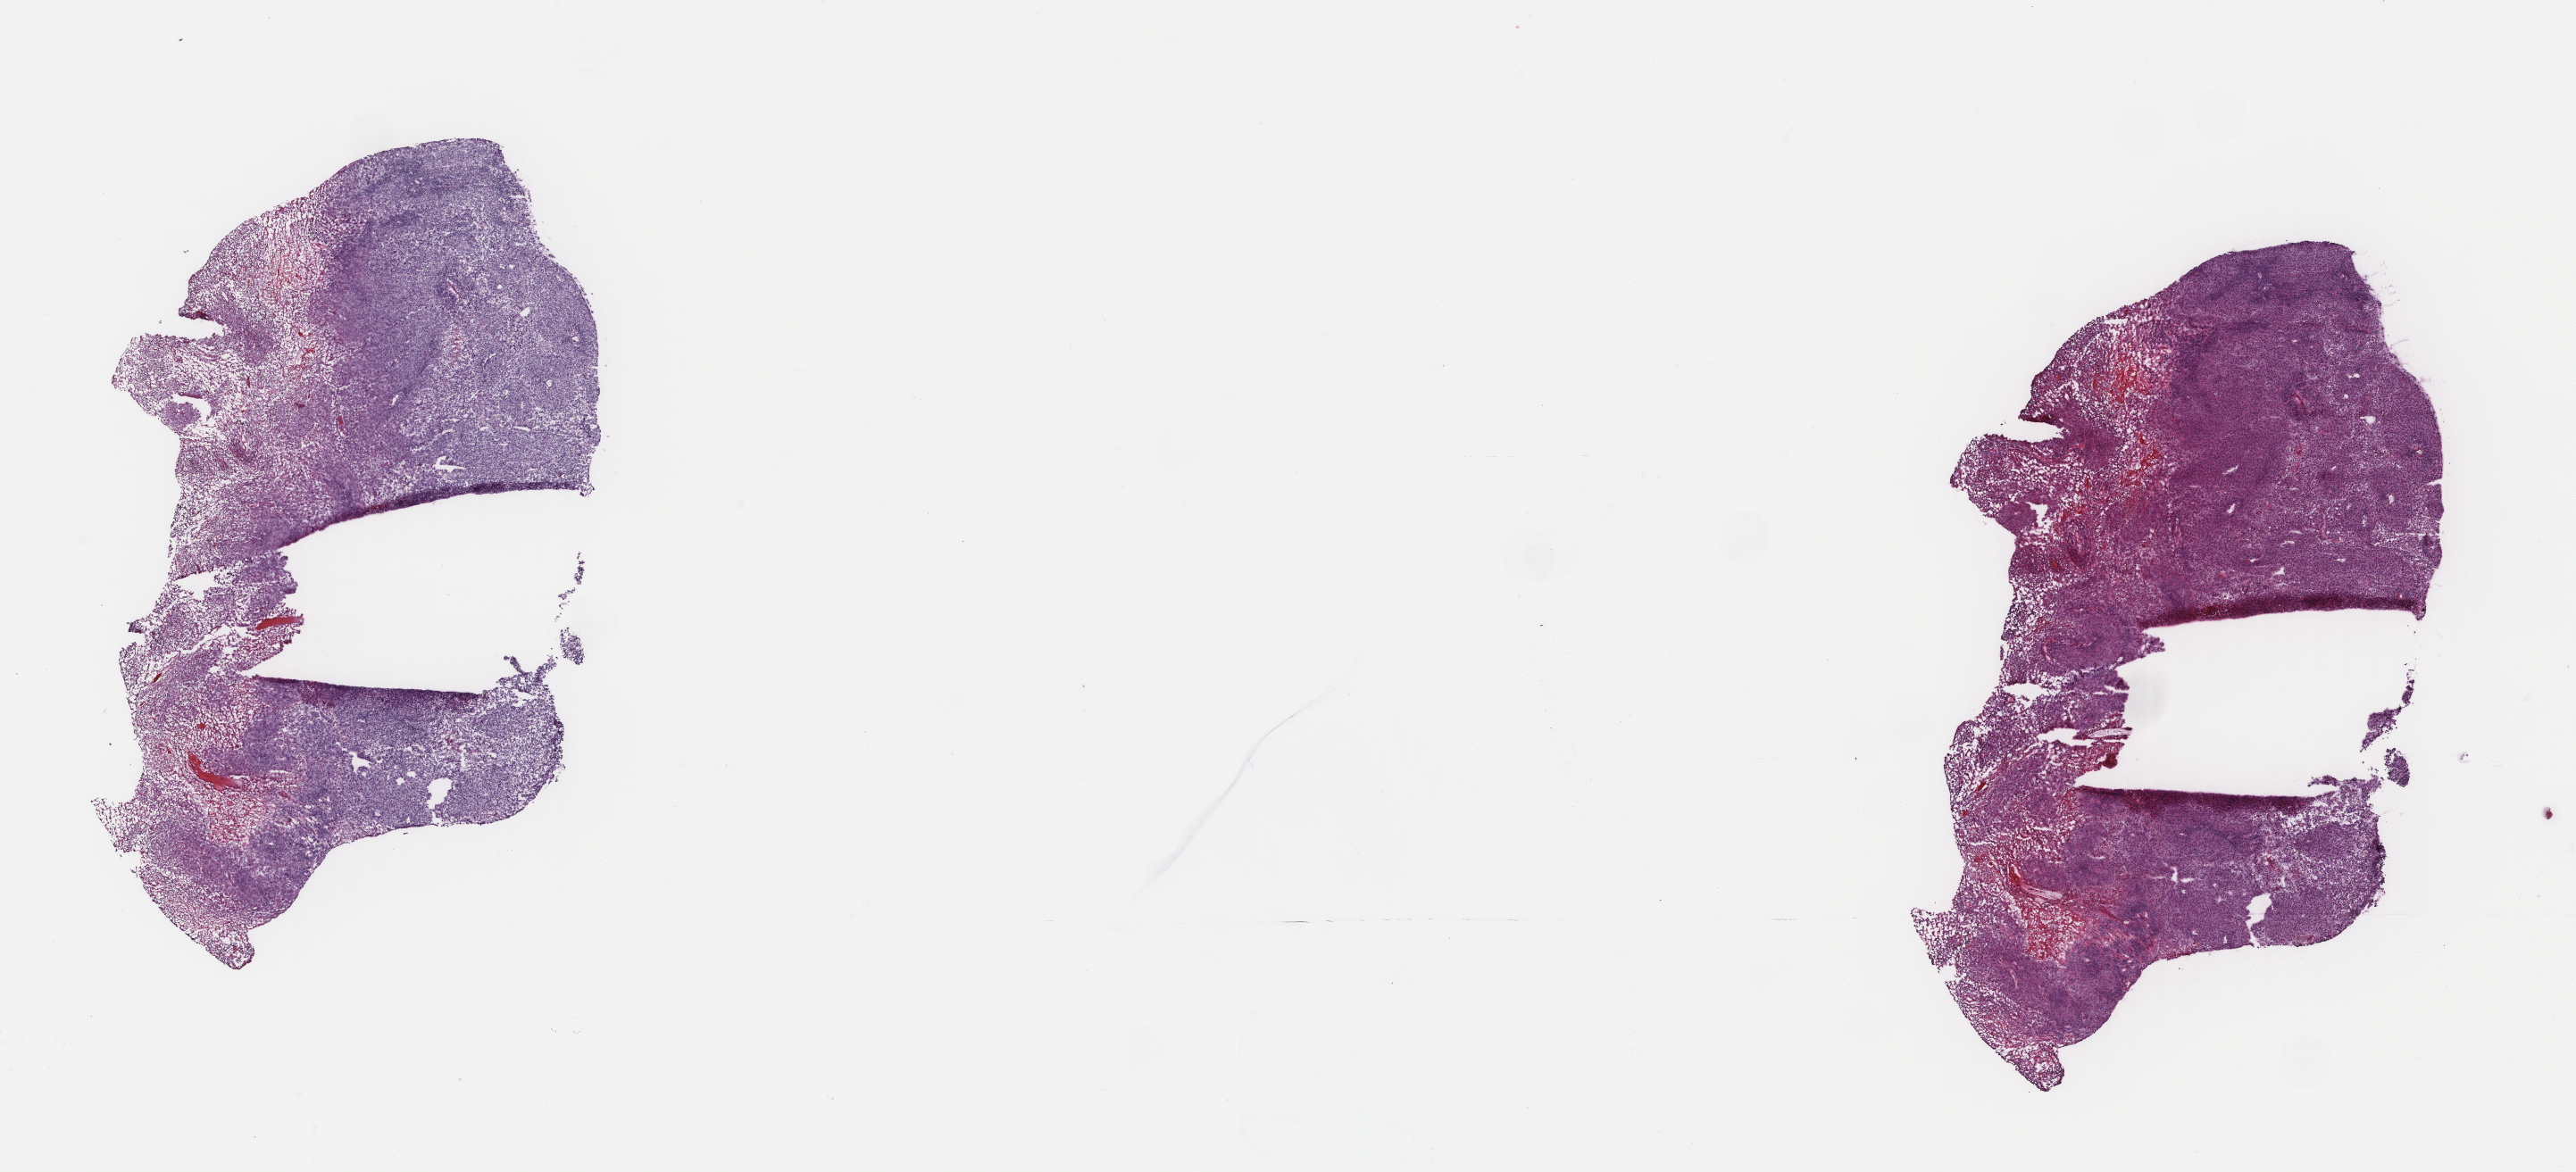
Digitized Hematoxylin and eosin (H&E) stained tissue section (whole slide), low-resolution overview of the scanned area, about 22.9 x 10.4 mm. Frozen section from the top of the tissue portion. Metastatic tumour sample, sampled site: pelvis. Female patient; age at initial diagnosis 46 years. Slide review estimates, as recorded: tumour cells 95%, tumour nuclei 95%.
This section: metastatic tumour tissue. Patient diagnosis: Malignant melanoma, NOS.